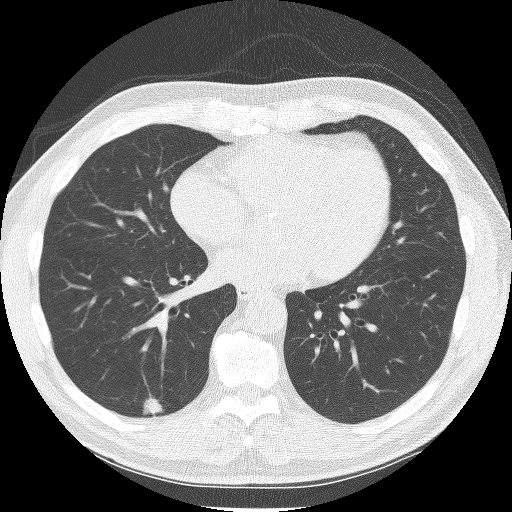
Low-dose screening chest CT, one axial slice; position 64 of 150 along the scan axis; reconstruction kernel BONE; 120 kVp; lung window (W 1500 / L -600 HU); 2.5 mm slice thickness; 512 × 512 image matrix, field of view 335 × 335 mm.
Annotated regions visible in this slice (expert manual segmentation):
- lesion 1 (tumor, lower lobe of right lung): bounding box [x1, y1, x2, y2] px = [143, 396, 162, 416]